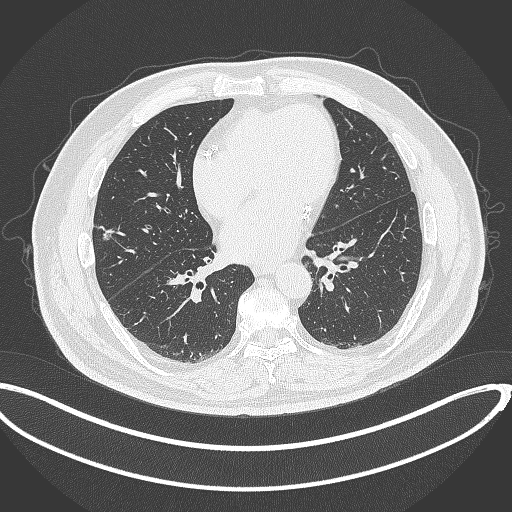
Chest CT, one axial slice; reconstruction kernel B70f; 120 kVp; lung window (W 1500 / L -600 HU); 1 mm slice thickness; 512 × 512 image matrix, field of view 427 × 427 mm. Patient: male, 68 years. From the clinical record (not read from this slice): clinical TNM (as recorded): T1c N0 M0; histopathological grade: G2.
Outlined on this slice (bounding box drawn by a radiologist):
- lung tumour (recorded histology: adenocarcinoma): bounding box [x1, y1, x2, y2] px = [99, 226, 116, 241]